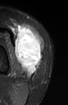
MRI of an extremity soft-tissue mass, one axial slice; position 29 of 52 along the scan axis; STIR; MR volume resampled by the dataset authors to the PET/CT grid (not the native acquisition matrix); 68 × 105 image matrix, field of view 66 × 103 mm. Female patient. From the clinical record (not read from this slice): histological type: spindle cell suggestive of biphasic synovial sarcoma; grade: intermediate; site of the primary tumour: left knee.
Annotated regions visible in this slice (expert contour drawn on MRI and transferred to this co-registered scan by the dataset authors):
- gross tumour volume including surrounding oedema: bounding box (x1, y1, x2, y2) in pixels: (12, 25, 43, 76)
- gross tumour volume (mass): (14, 27, 43, 76)